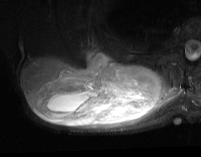
MRI of an extremity soft-tissue mass, one axial slice; slice 33 of 74 in the series (ordered by position); STIR; MR volume resampled by the dataset authors to the PET/CT grid (not the native acquisition matrix); 3.27 mm slice thickness; 201 × 157 image matrix. Male patient. Case-level facts recorded for this patient, not image findings: histological type: pleiomorphic spindle cell undifferentiated; grade: high; site of the primary tumour: right parascapusular.
Annotated regions visible in this slice (expert contour drawn on MRI and transferred to this co-registered scan by the dataset authors):
- gross tumour volume including surrounding oedema: box from (x=21, y=54) to (x=180, y=129) px
- gross tumour volume (mass): (x=21, y=54)–(x=162, y=127)